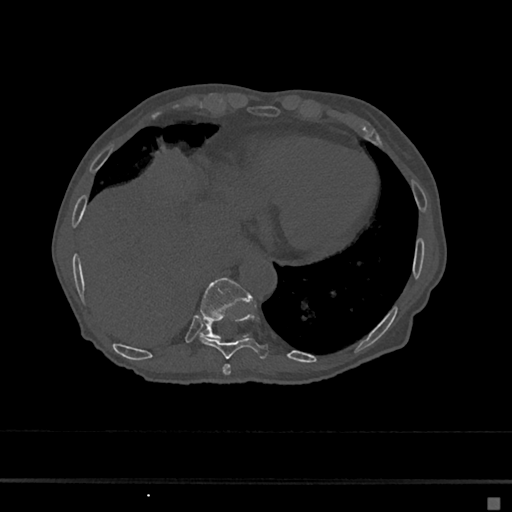
CT including the spine, one axial slice. Slice 258 of 797 in the series (ordered by position). Reconstruction kernel Br40s/3. Bone window (W 1800 / L 400 HU). 0.5 mm slice thickness. 512 × 512 image matrix. Patient: female, 68 years. Case-level facts recorded for this patient, not image findings: primary cancer: renal.
Outlined on this slice (semi-automatically segmented with operator editing):
- T10 vertebra: bounding box <200,278,251,339> (left, top, right, bottom; pixels)
- T8 vertebra: <222,364,231,375>
- T9 vertebra: <199,312,270,359>